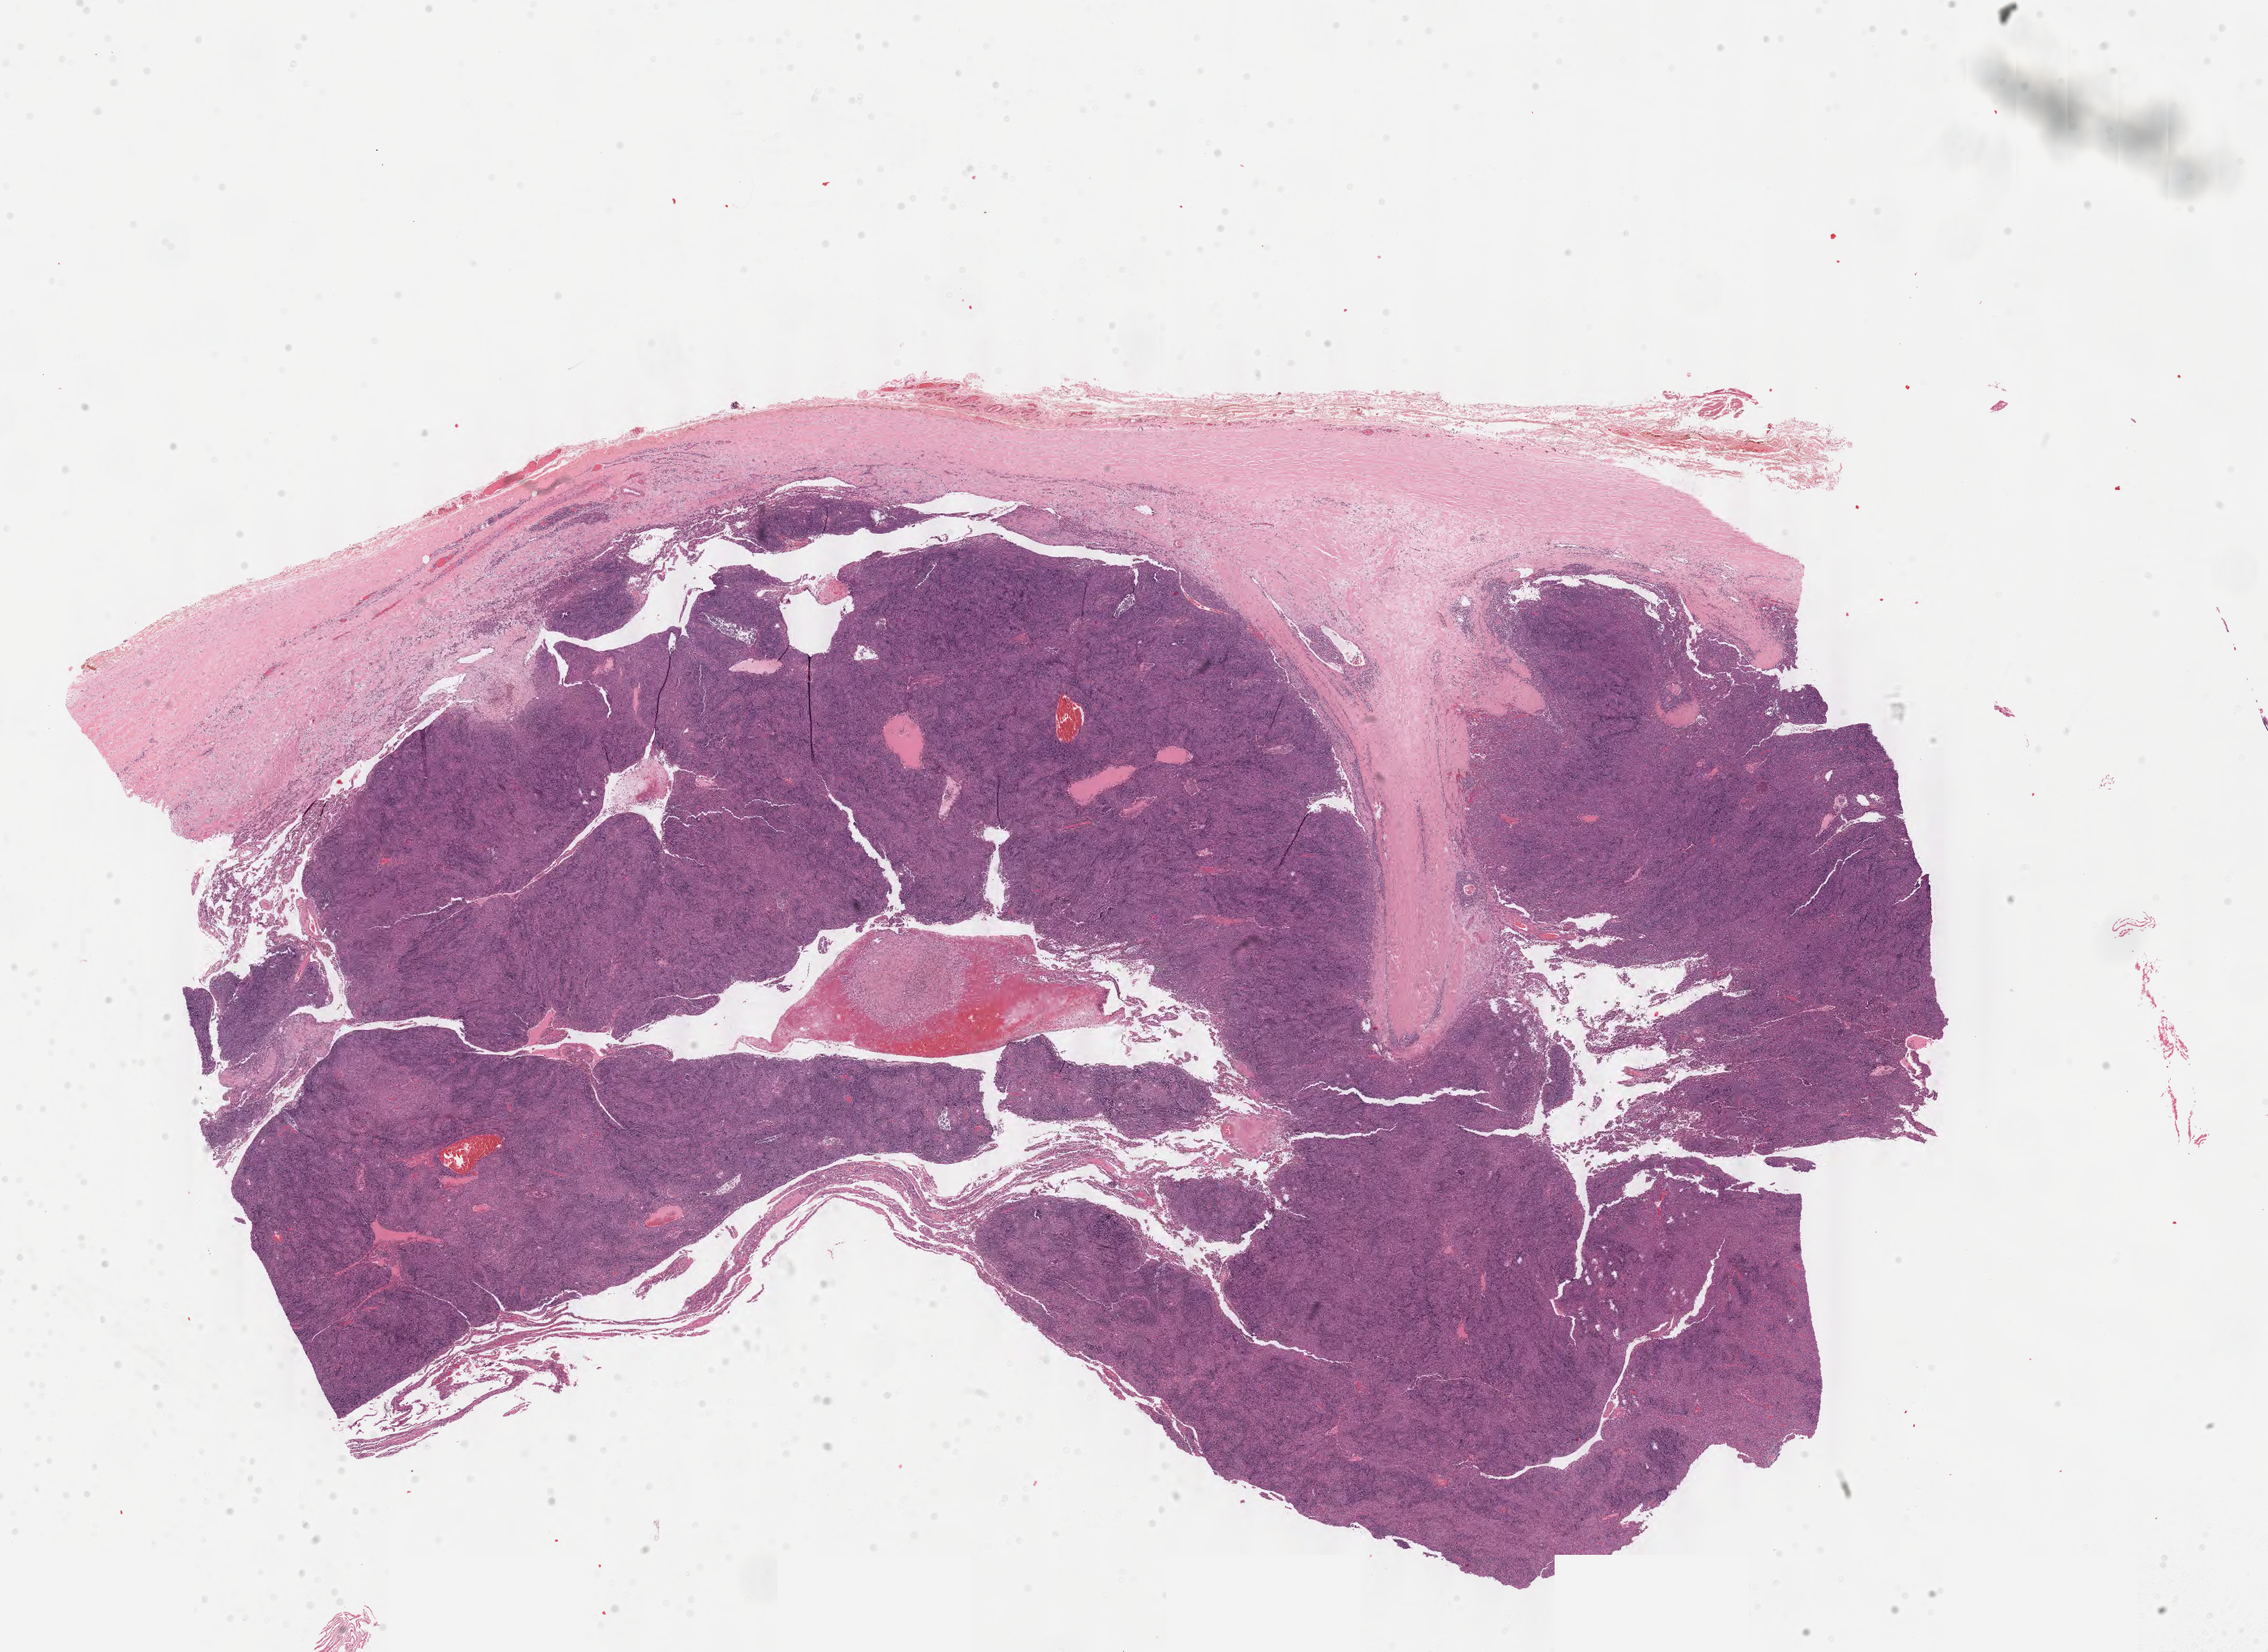
H&E-stained whole-slide image — whole scanned area (about 22.1 x 16.1 mm) shown as a low-resolution overview; formalin-fixed paraffin-embedded (FFPE) diagnostic section; thymus, primary tumour sample. Male, age 17 years at initial diagnosis.
• diagnosis: Thymoma, type B2, malignant